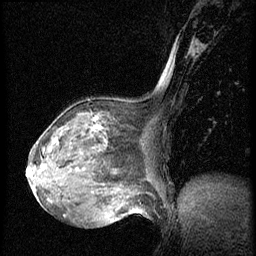
Breast MRI (dynamic contrast-enhanced), one sagittal slice; dynamic contrast-enhanced series, image 2 of 3 at this slice position (ordered by acquisition); 1.5 T; TE 4.2 ms, TR 20.4 ms; 256 × 256 image matrix, field of view 200 × 200 mm. Patient: female, 64 years. From the clinical record (not read from this slice): setting: breast cancer imaged before/during neoadjuvant chemotherapy; receptor status: HR-positive, HER2-negative.
Structures marked on this image (semi-automatic segmentation, software-assisted and operator-edited):
- analysis volume of interest (the breast-tissue region the enhancement analysis was run in; not a lesion): bounding box [x1, y1, x2, y2] px = [48, 101, 142, 186]
- tumour enhancement mask (voxels above the 70 % enhancement threshold inside the analysis volume of interest): [93, 117, 101, 129]